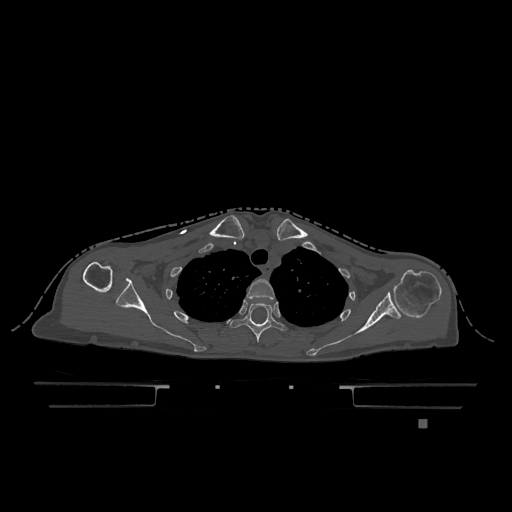
CT including the spine, one axial slice. Slice 933 of 1317 in the series (ordered by position). Bone window (W 1800 / L 400 HU). 0.5 mm slice thickness. 512 × 512 image matrix, field of view 500 × 500 mm. Patient: female, 74 years. Case-level facts recorded for this patient, not image findings: primary cancer: lung.
Annotated regions visible in this slice (semi-automatically segmented with operator editing):
- T2 vertebra: bounding box [x1, y1, x2, y2] px = [246, 279, 275, 300]
- T3 vertebra: [230, 303, 288, 342]